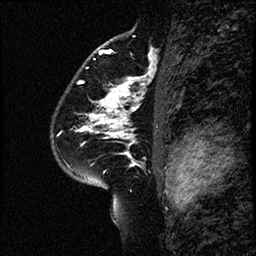
Breast MRI (dynamic contrast-enhanced), one sagittal slice; position 41 of 60 along the scan axis; dynamic contrast-enhanced study with each time point stored as its own series, time point 2 of 4 at this slice position (early post-contrast, ordered by acquisition time); 1.5 T; TE 4.2 ms, TR 17.6 ms; 2 mm slice thickness; 256 × 256 image matrix, field of view 200 × 200 mm. Female patient, age 43 years. Case-level facts recorded for this patient, not image findings: setting: breast cancer imaged before/during neoadjuvant chemotherapy.
Outlined on this slice (semi-automatically segmented with operator editing):
- analysis volume of interest (the breast-tissue region the enhancement analysis was run in; not a lesion): bounding box <55,67,169,191> (left, top, right, bottom; pixels)
- tumour enhancement mask (voxels above the 100 % enhancement threshold inside the analysis volume of interest): <84,82,136,137>